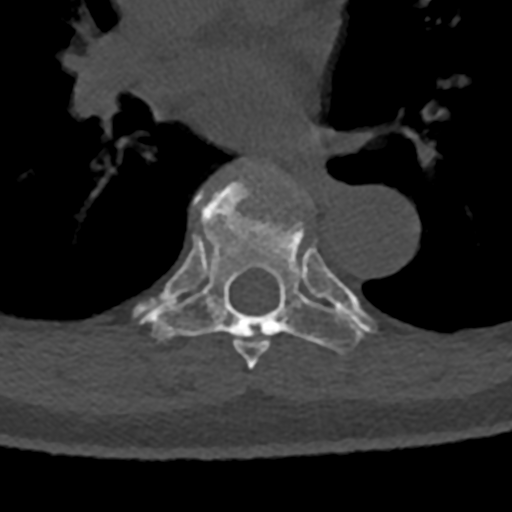
CT including the spine, one axial slice; slice 775 of 797 in the series (ordered by position); bone window (W 1800 / L 400 HU); 512 × 512 image matrix. Male patient, age 74 years. Case-level facts recorded for this patient, not image findings: primary cancer: renal.
Structures marked on this image (semi-automatic segmentation, software-assisted and operator-edited):
- T6 vertebra: bounding box [x1, y1, x2, y2] px = [186, 192, 270, 370]
- T7 vertebra: [133, 179, 372, 353]